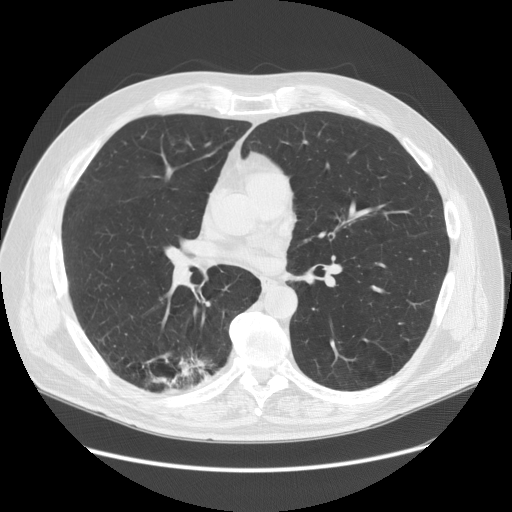
Chest CT (low-dose screening protocol), one axial image, baseline screening round, lung window (W 1500 / L -600 HU), slice 75 of 149 in the series. Male, age 68 years at enrolment. Former smoker at enrolment.
Expert-annotated lung lesion, bounding box (x1, y1, x2, y2) in pixels: (127, 341, 225, 413). Screening reader's record for this exam (one nodule recorded; not confirmed to be the boxed lesion): non-calcified nodule or mass ≥4 mm, right lower lobe, 37 × 20 mm, spiculated (stellate) margins, soft tissue attenuation. Lung cancer was diagnosed 24 days after this screen: adenosquamous carcinoma, right lower lobe, poorly differentiated (G3), stage IIIA (AJCC 6th edition), 30 mm at pathology.